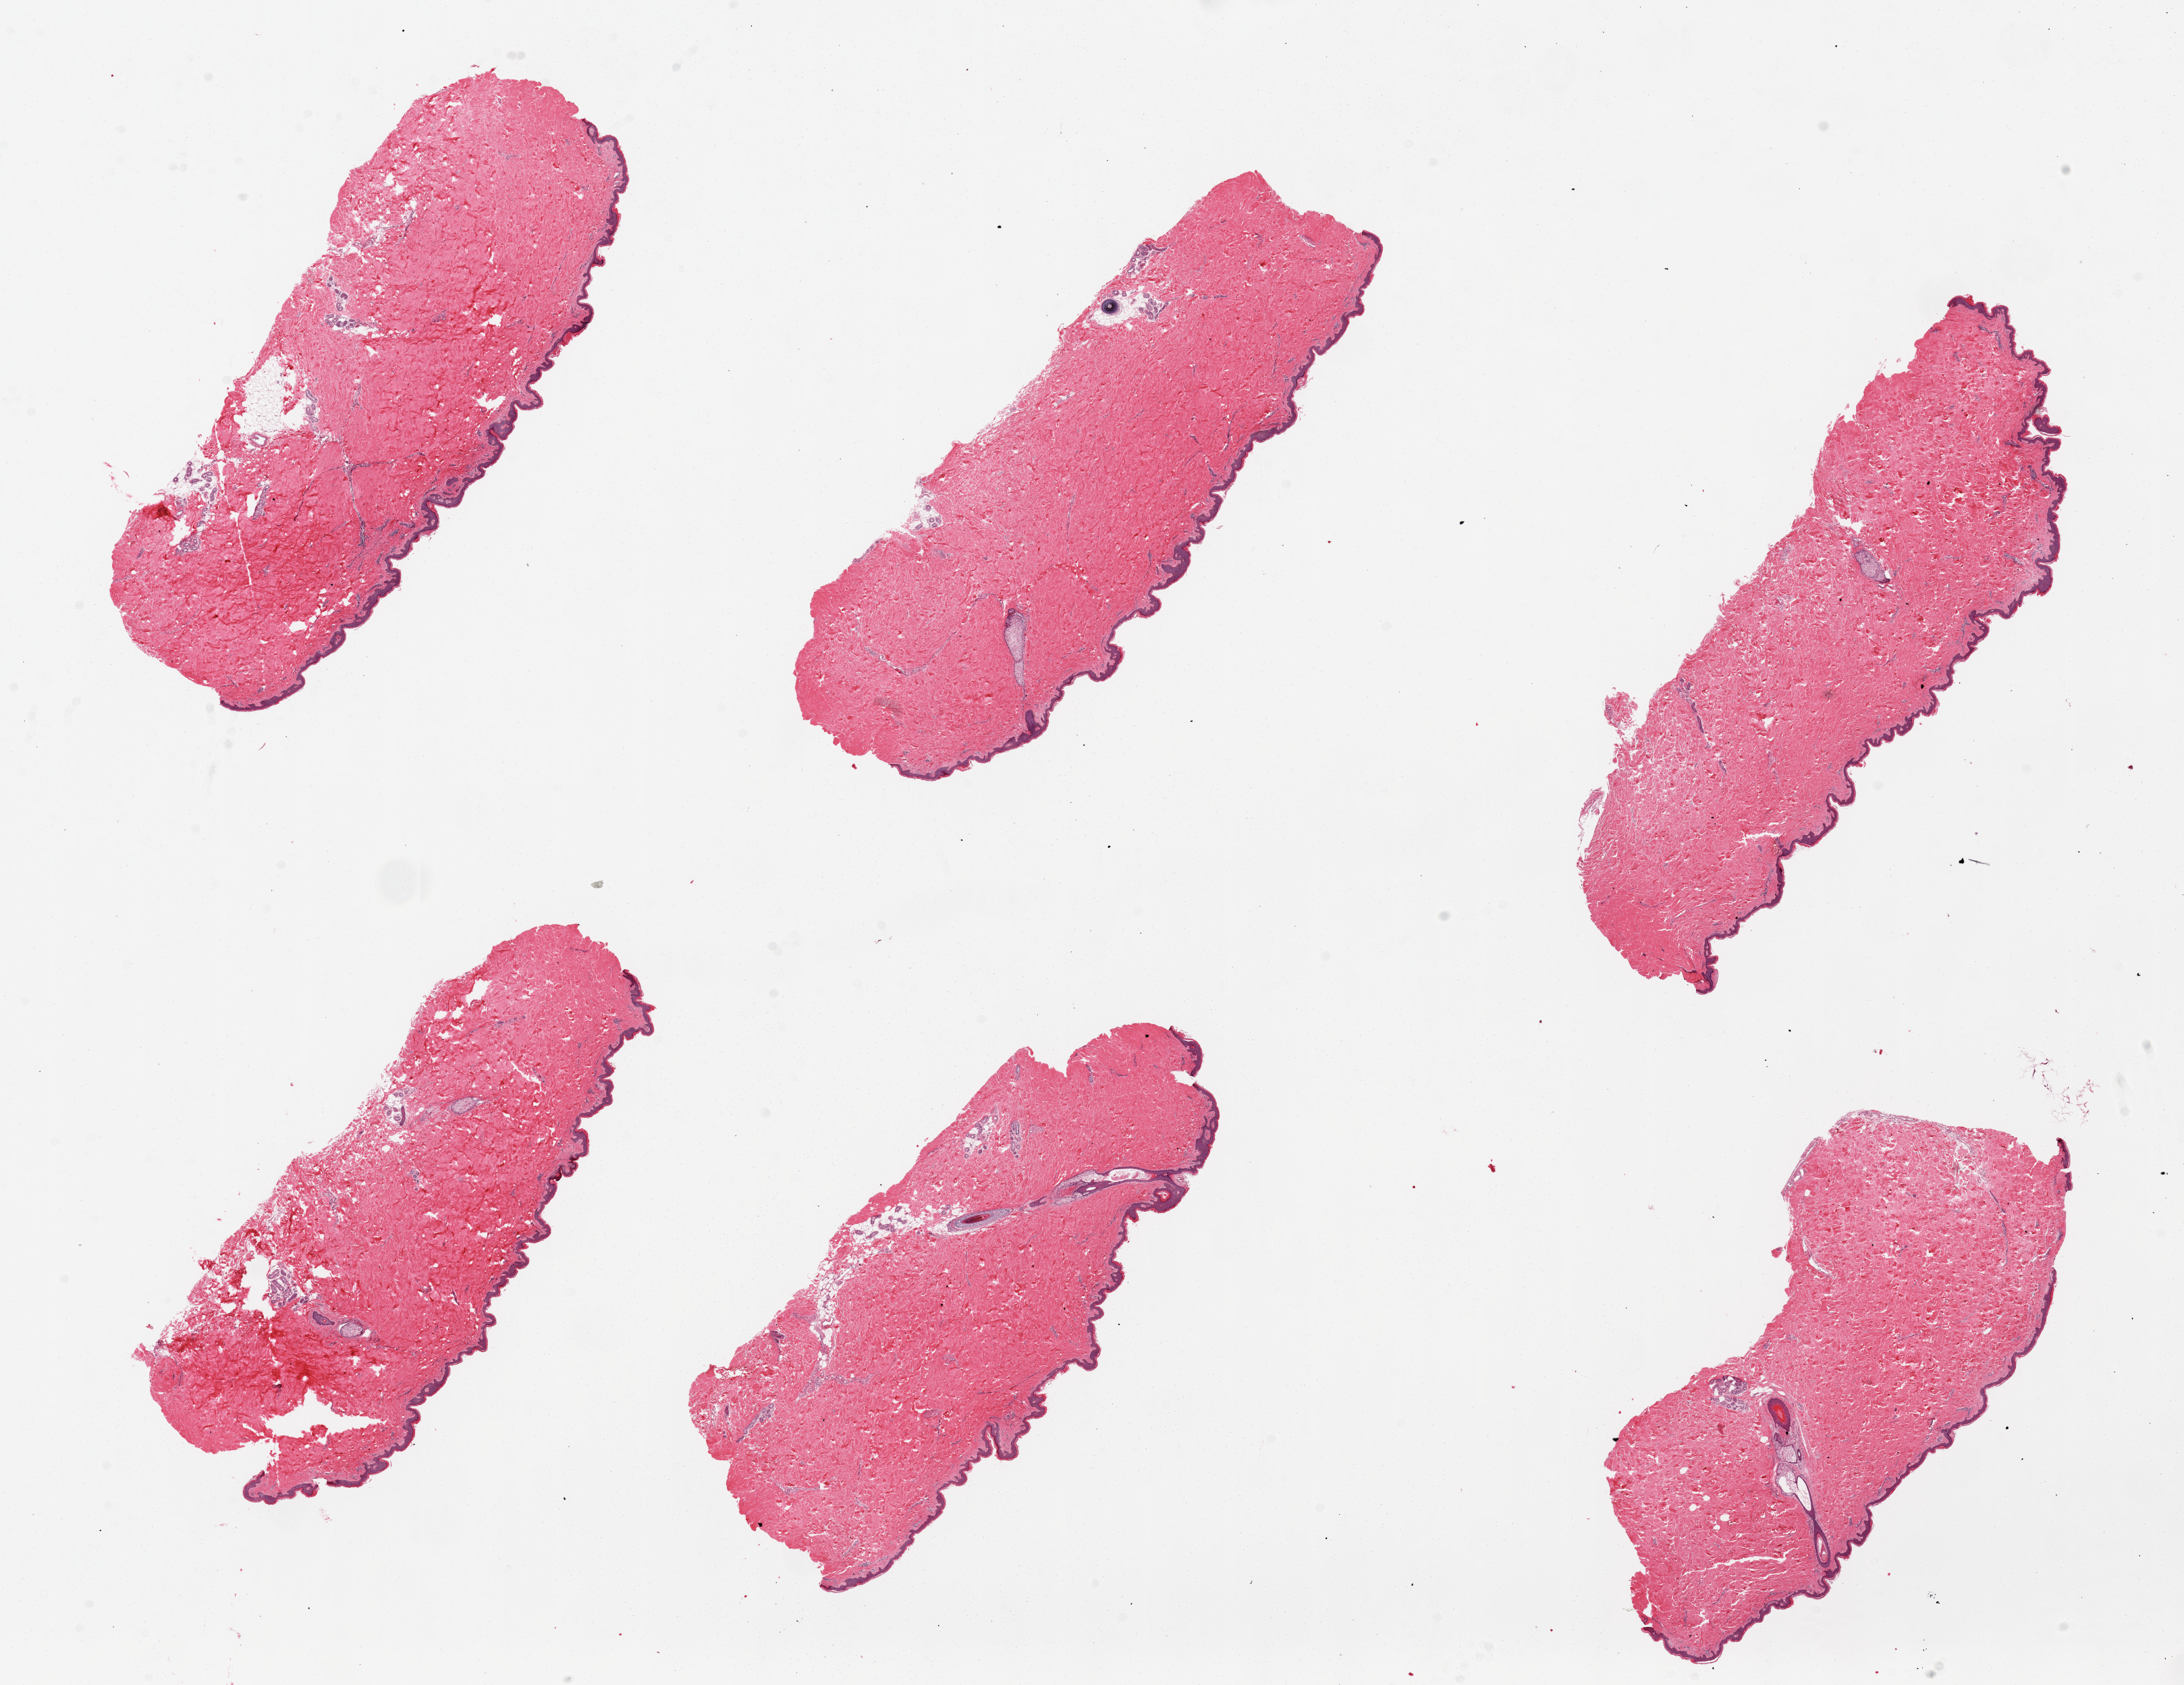
Digitized H&E-stained section, low-resolution overview of the scanned area, about 25.6 x 19.7 mm (slide scanned at 20x); PAXgene-fixed paraffin-embedded (PFPE) section; sampled site (target tissue): skin of suprapubic region; donor tissue sample. Donor: male.
Review note (as recorded): 6 pieces; well-trimmed. Squamous epithelium is ~ 1% of thickness. Dermatophytes identified.